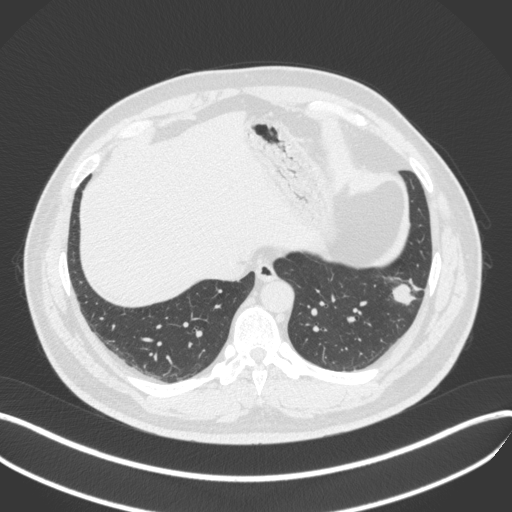
Chest CT, one axial slice. Position 112 of 420 along the scan axis. Reconstruction kernel B31f. Lung window (W 1500 / L -600 HU). 1 mm slice thickness. 512 × 512 image matrix. Male patient, age 39 years. From the clinical record (not read from this slice): clinical TNM (as recorded): T2a N0 M0.
Annotated regions visible in this slice (rectangle marked by the reading radiologist):
- lung tumour (recorded histology: adenocarcinoma): bounding box <389,274,425,311> (left, top, right, bottom; pixels)